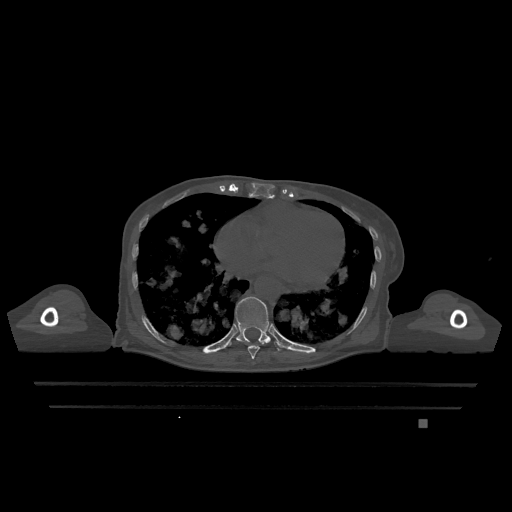
CT including the spine, one axial slice; slice 664 of 1317 in the series (ordered by position); bone window (W 1800 / L 400 HU); 0.5 mm slice thickness; 512 × 512 image matrix, field of view 500 × 500 mm. Female patient, age 74 years. Case-level facts recorded for this patient, not image findings: primary cancer: lung; vertebrae with lytic lesions (as recorded): T1, T4, T5, T6, L4, L5.
Structures marked on this image (semi-automatically segmented with operator editing):
- T10 vertebra: bounding box [x1, y1, x2, y2] px = [230, 296, 280, 351]
- T9 vertebra: [247, 342, 264, 359]